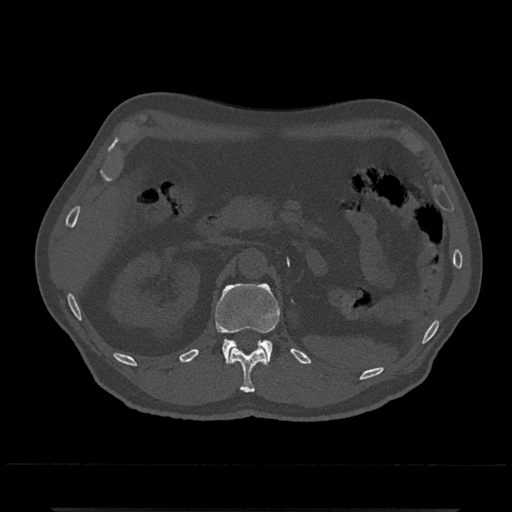
CT including the spine, one axial slice; position 392 of 797 along the scan axis; bone window (W 1800 / L 400 HU); 0.5 mm slice thickness; 512 × 512 image matrix. Patient: male, 67 years. From the clinical record (not read from this slice): primary cancer: prostate.
Outlined on this slice (semi-automatically segmented with operator editing):
- L1 vertebra: box from (x=215, y=283) to (x=280, y=364) px
- T12 vertebra: (x=230, y=346)–(x=268, y=393)